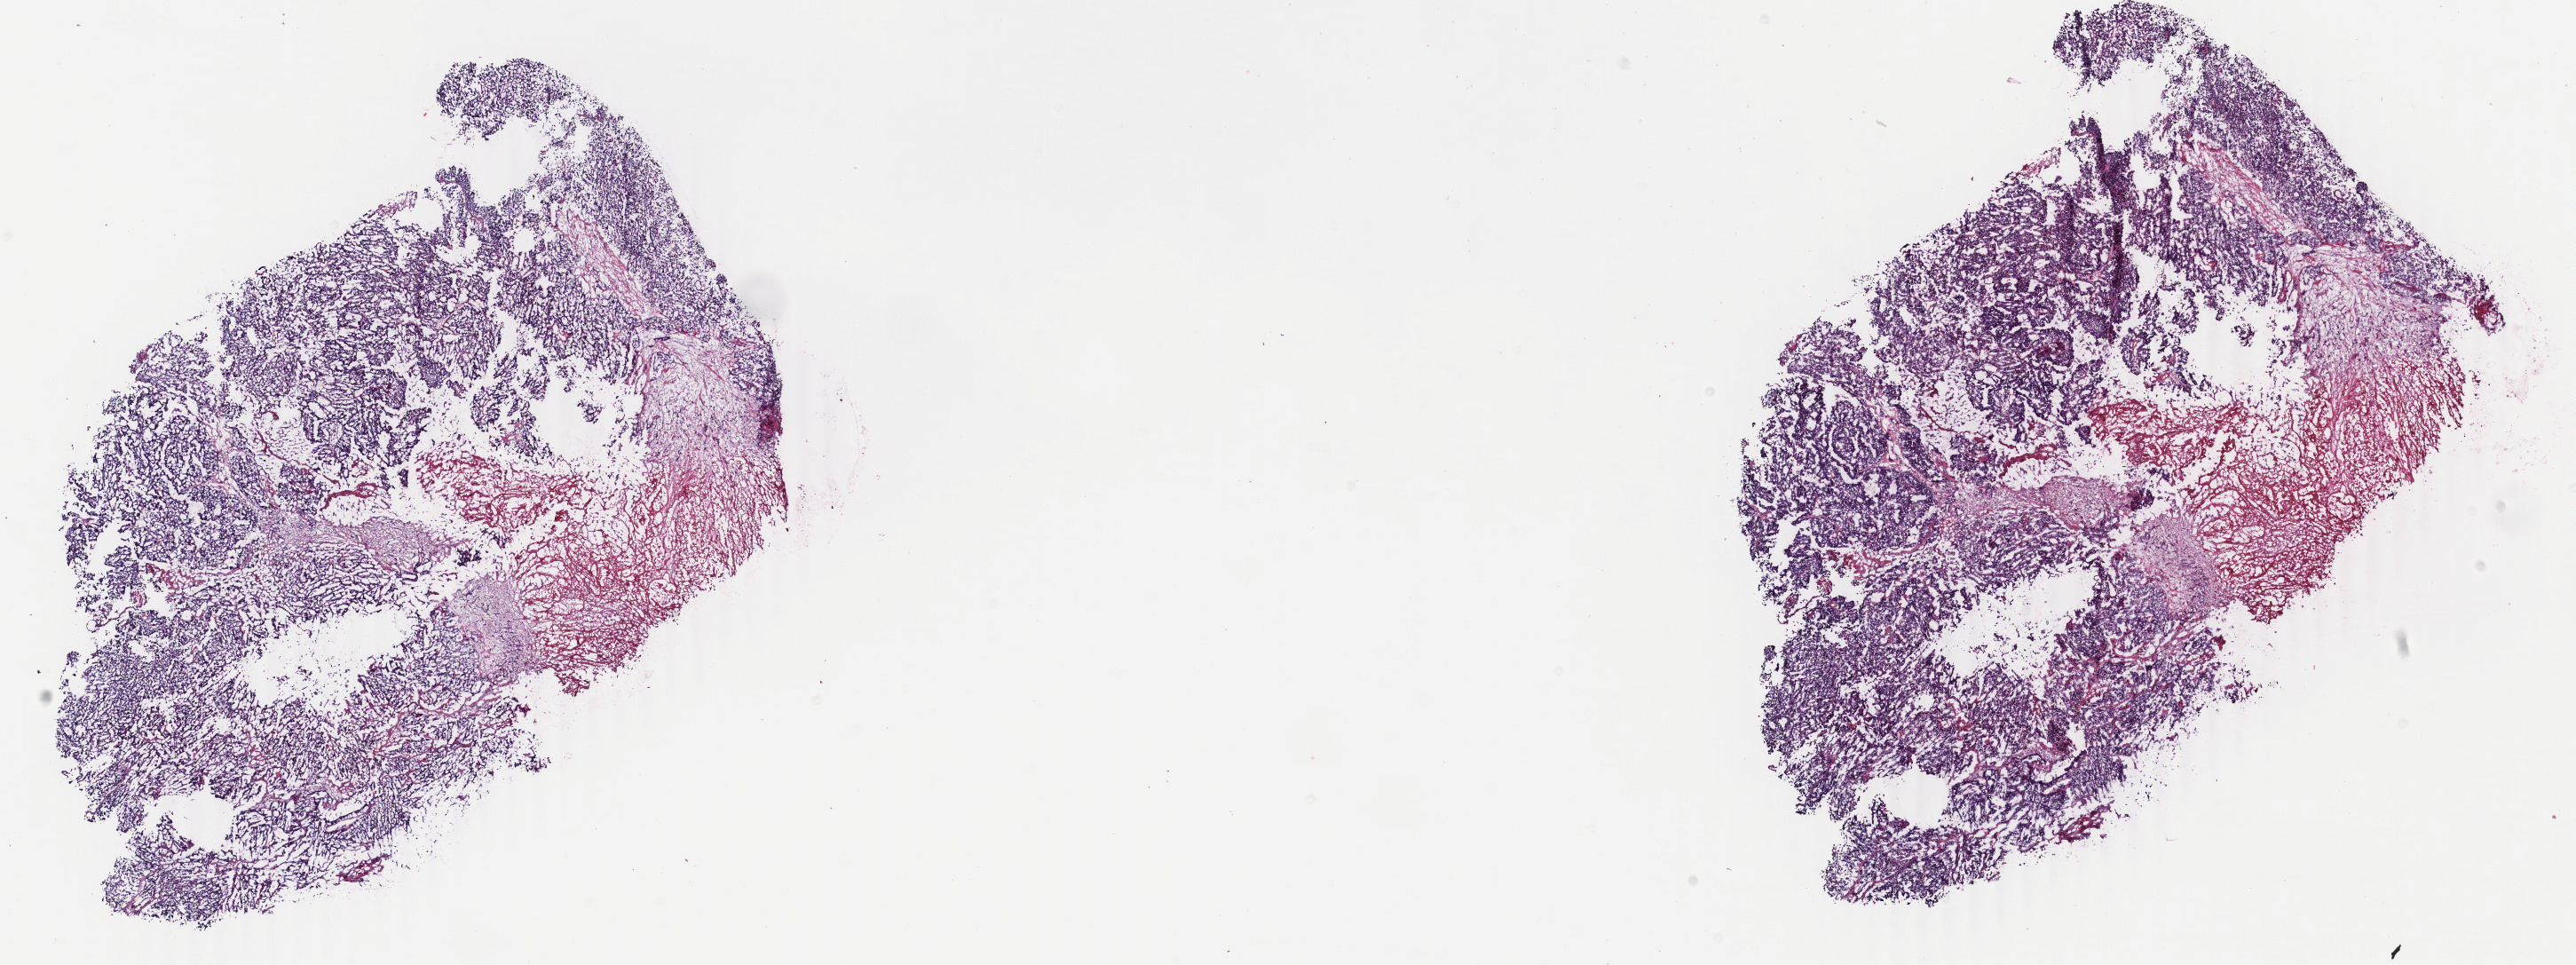
Digitized H&E tissue section (whole slide) — shown as a low-resolution overview of the whole scanned area (about 23.1 x 8.6 mm, from a 40x scan). Frozen section from the bottom of the tissue portion. Primary tumour sample from the uterus. Female patient; age at initial diagnosis 51 years. Histologic grade: G2 (moderately differentiated). Slide review estimates, as recorded: tumour cells 70%, tumour nuclei 80%, normal cells 0%, stromal cells 15%, necrosis 15%. Inflammatory infiltration, as recorded: lymphocyte infiltration 0%, monocyte infiltration 0%, neutrophil infiltration 0%.
* histologic diagnosis: Endometrioid adenocarcinoma, NOS (endometrium)
* FIGO stage: IB